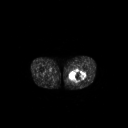
FDG PET of an extremity soft-tissue mass (from a PET/CT study), one axial slice. 3.27 mm slice thickness. 128 × 128 image matrix. Male patient, age 44 years. From the clinical record (not read from this slice): histological type: undifferentiated pleomorphic liposarcoma; grade: high; site of the primary tumour: left thigh.
Annotated regions visible in this slice (expert contour drawn on MRI and transferred to this co-registered scan by the dataset authors):
- gross tumour volume including surrounding oedema: bounding box <67,69,86,83> (left, top, right, bottom; pixels)
- gross tumour volume (mass): <69,69,86,81>